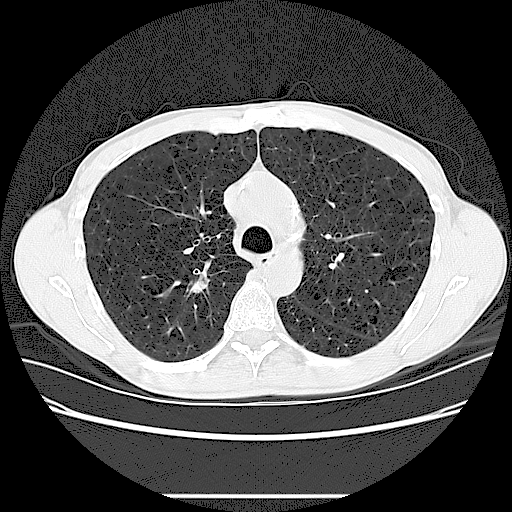
Low-dose screening chest CT, one axial slice; slice 91 of 131 in the series (ordered by position); lung window (W 1500 / L -600 HU); 512 × 512 image matrix, field of view 360 × 360 mm.
Annotated regions visible in this slice (manually delineated by an expert):
- lesion 1 (tumor, upper lobe of right lung): box from (x=190, y=280) to (x=206, y=294) px